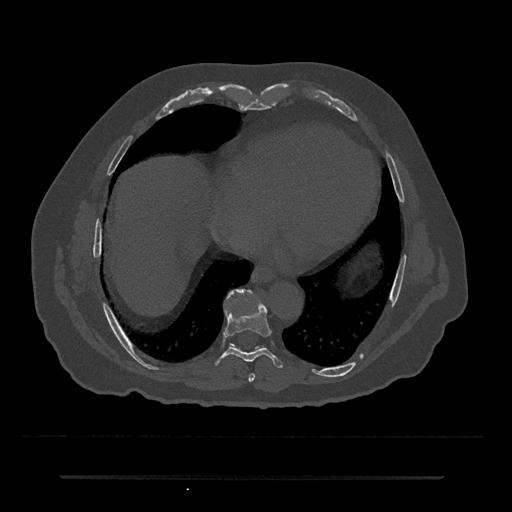
CT including the spine, one axial slice. Slice 323 of 797 in the series (ordered by position). Reconstruction kernel Br40s/3. Bone window (W 1800 / L 400 HU). 512 × 512 image matrix. Male patient, age 69 years. Case-level facts recorded for this patient, not image findings: primary cancer: prostate.
Outlined on this slice (semi-automatic segmentation, software-assisted and operator-edited):
- T7 vertebra: box from (x=248, y=373) to (x=255, y=382) px
- T8 vertebra: (x=215, y=302)–(x=283, y=368)
- T9 vertebra: (x=230, y=289)–(x=248, y=299)